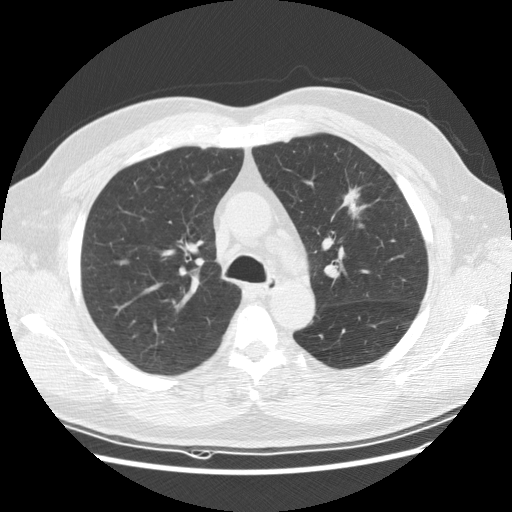
Chest CT (low-dose screening protocol), one axial image, baseline annual screen, lung window (W 1500 / L -600 HU), standard (soft-tissue) reconstruction kernel (STANDARD), slice 46 of 152 in the series. Male, age 65 years at enrolment. Current smoker at enrolment.
- Lesion marked by an expert reader, bounding box [x1, y1, x2, y2] px = [323, 179, 382, 232].
- The screening reader recorded 2 non-calcified nodules or masses ≥4 mm on this exam; which of them this box marks is not recorded.